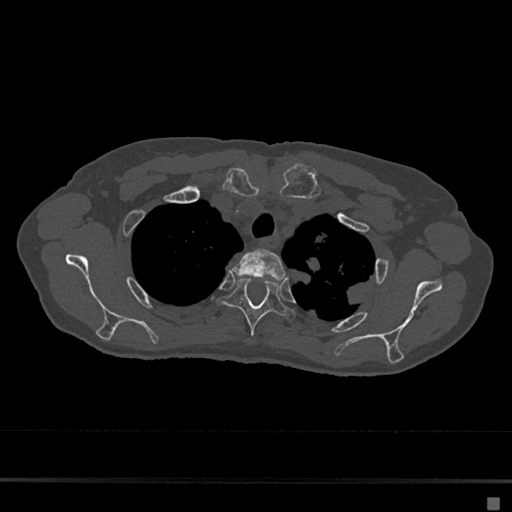
CT including the spine, one axial slice; reconstruction kernel Br40s/3; 120 kVp; bone window (W 1800 / L 400 HU); 512 × 512 image matrix. Female patient, age 68 years. From the clinical record (not read from this slice): primary cancer: renal.
Annotated regions visible in this slice (semi-automatic segmentation, software-assisted and operator-edited):
- T2 vertebra: bounding box (x1, y1, x2, y2) in pixels: (232, 249, 287, 281)
- T3 vertebra: (219, 278, 295, 336)